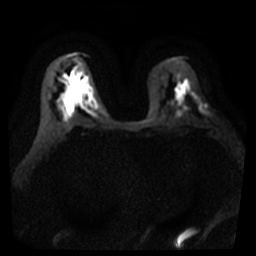
Breast MRI, one axial slice; position 22 of 40 along the scan axis; diffusion-weighted series; image 2 of 4 stored at this slice position (different b-values; order by instance number); 3 T; 256 × 256 image matrix. Female patient.
Outlined on this slice (expert manual segmentation):
- tumour on diffusion-weighted imaging: bounding box <202,105,209,115> (left, top, right, bottom; pixels)